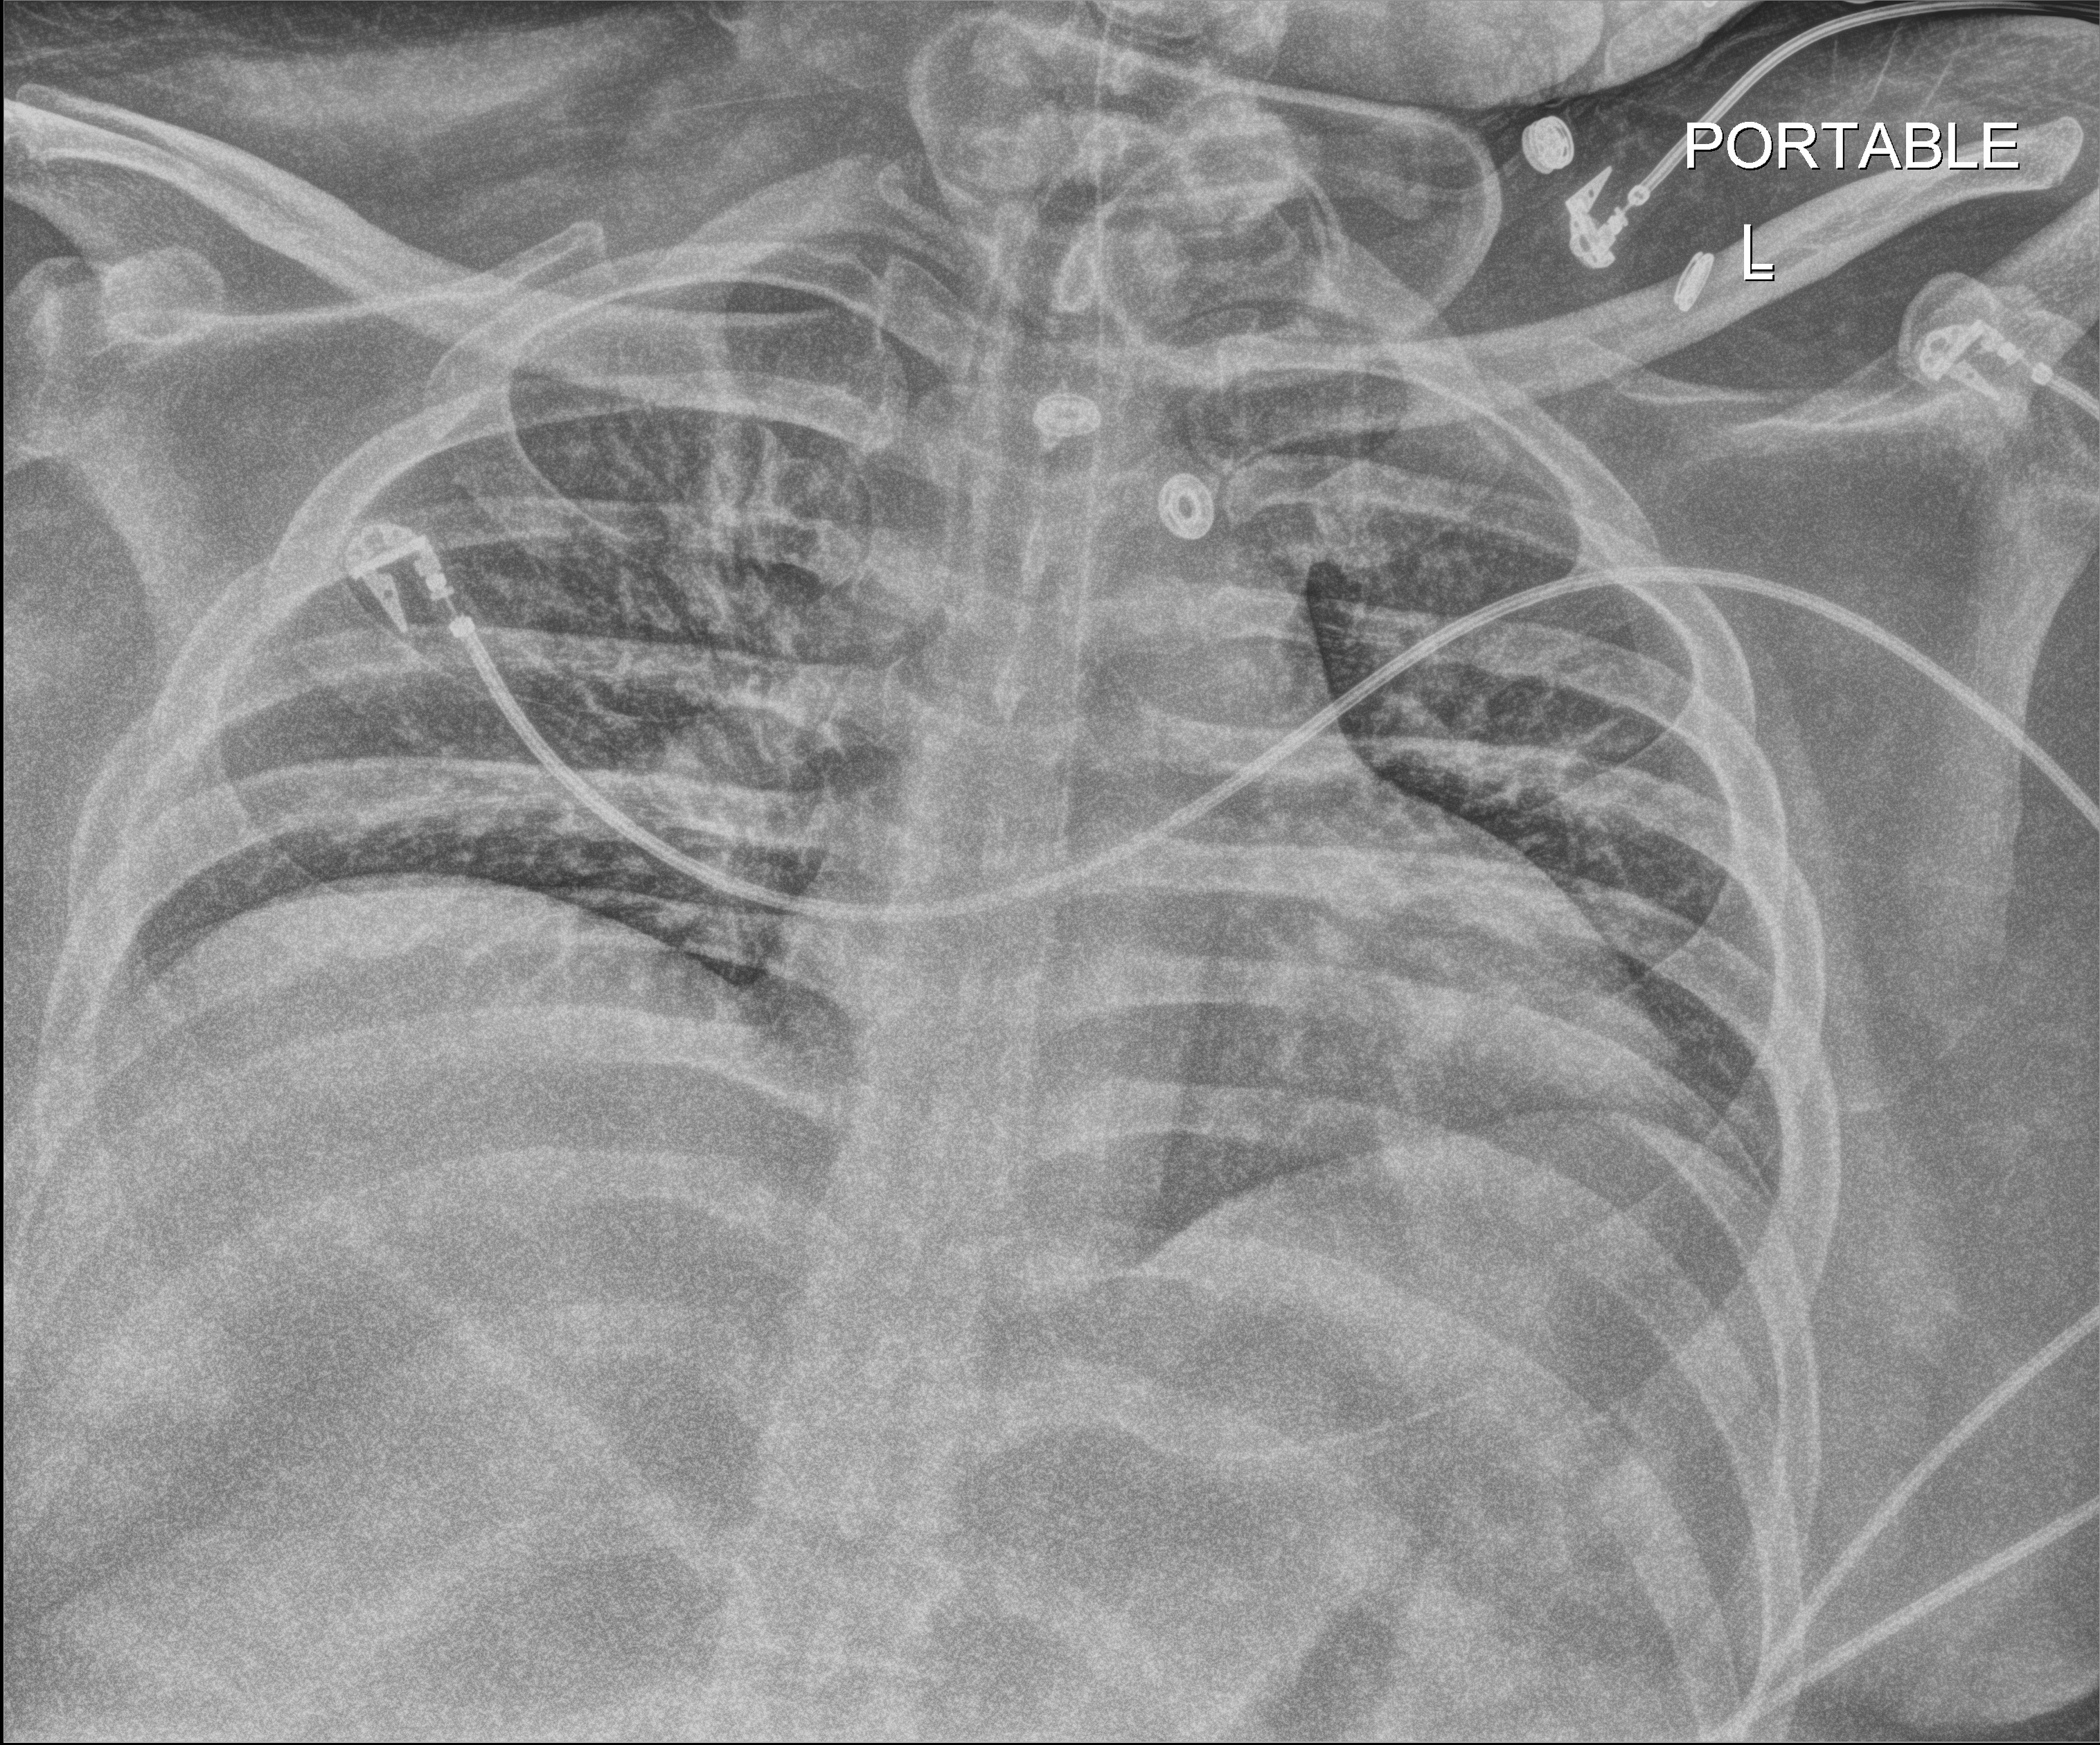
Chest X-ray (portable); anteroposterior (AP) projection. Male patient hospitalised with COVID-19, age 18–59 years.
Admission-level facts for this patient (not findings on this image; timing relative to this image not recorded): smoking status (admission record): never; mechanically ventilated during this hospital stay: yes.